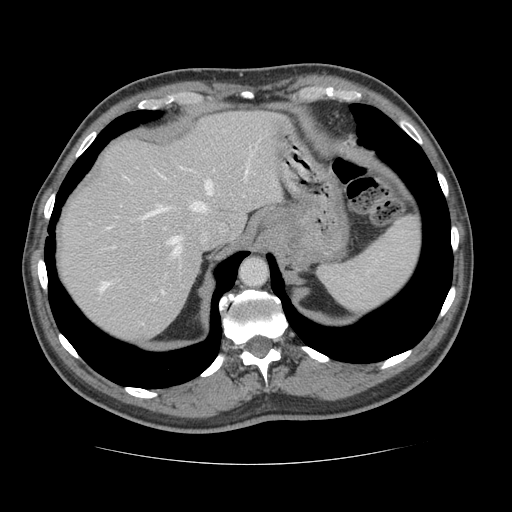
Contrast-enhanced abdominal CT, one axial slice; slice 104 of 134 in the series (ordered by position); reconstruction kernel STANDARD; 120 kVp; intravenous contrast given; soft-tissue window (W 400 / L 40 HU); 2.5 mm slice thickness; 512 × 512 image matrix. Male patient, age 68 years. From the clinical record (not read from this slice): diagnosis: colorectal cancer liver metastases, imaged before liver resection; multiple liver metastases: yes.
Outlined on this slice (outlined manually by an expert reader):
- hepatic veins: bounding box [x1, y1, x2, y2] px = [99, 152, 253, 294]
- liver: [58, 110, 281, 342]
- planned liver remnant (the part of the liver to remain after resection): [58, 111, 281, 320]
- portal vein (with intrahepatic branches): [113, 246, 155, 299]